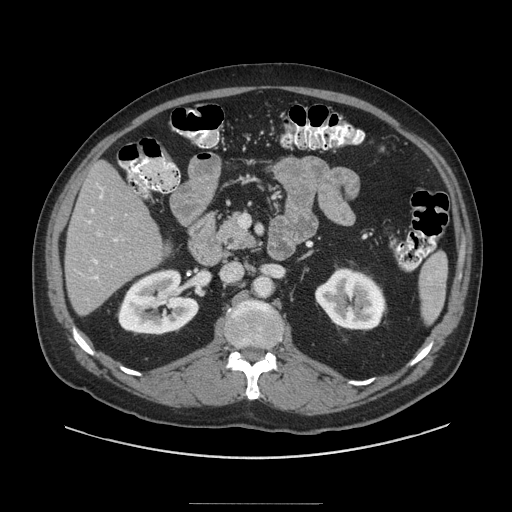
Contrast-enhanced abdominal CT (liver protocol), one axial slice; slice 41 of 91 in the series (ordered by position); reconstruction kernel STANDARD; 140 kVp; soft-tissue window (W 400 / L 40 HU); 2.5 mm slice thickness; 512 × 512 image matrix. Case-level facts recorded for this patient, not image findings: diagnosis: hepatocellular carcinoma (patient treated with transarterial chemoembolisation; whether this scan precedes or follows treatment is not stated here); TNM stage (as recorded): Stage-I; Child-Pugh class: A; tumour differentiation: well differentiated; tumour nodularity: uninodular.
Structures marked on this image (semi-automatically segmented with operator editing):
- liver parenchyma outside the tumour (the mass and vessels are separate outlines, so this box may not span the whole liver): bounding box (x1, y1, x2, y2) in pixels: (64, 160, 162, 314)
- liver vessels: (80, 184, 118, 280)